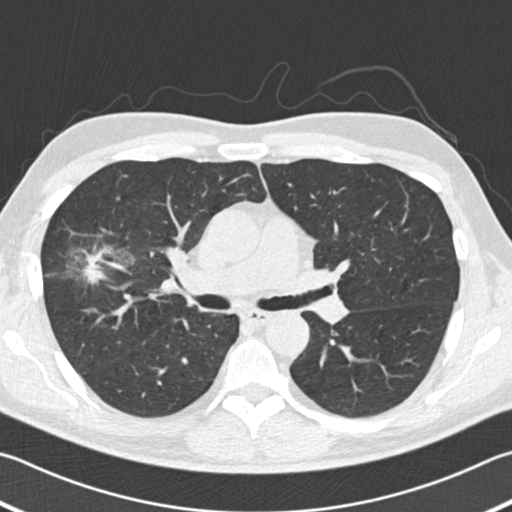
Chest CT (low-dose screening protocol), one axial image; second annual screen; lung window (W 1500 / L -600 HU); 2 mm slice thickness; 120 kVp. Male participant, aged 56 years at enrolment. Former smoker at enrolment.
Expert reader's lesion annotation, bounding box <49,233,135,298> (left, top, right, bottom; pixels). Reader record for this screening exam (exam-level; its link to the box is not recorded): non-calcified nodule or mass ≥4 mm, right upper lobe, 18 × 14 mm, spiculated (stellate) margins, soft tissue attenuation, pre-existing on the prior screen: yes; interval growth: yes.